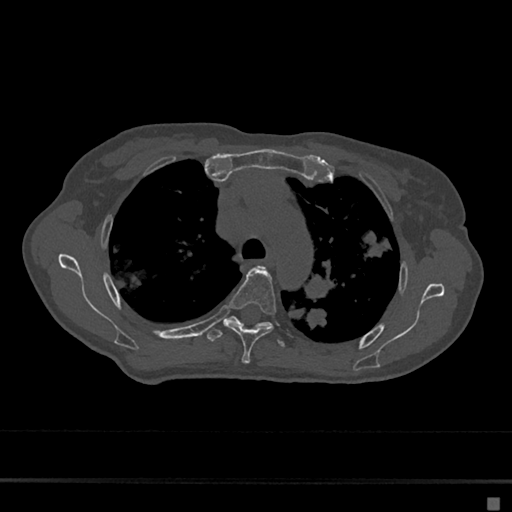
CT including the spine, one axial slice; slice 492 of 797 in the series (ordered by position); reconstruction kernel Br40s/3; bone window (W 1800 / L 400 HU); 0.5 mm slice thickness; 512 × 512 image matrix, field of view 360 × 360 mm. Female patient, age 68 years. Case-level facts recorded for this patient, not image findings: primary cancer: renal.
Outlined on this slice (semi-automatically segmented with operator editing):
- T4 vertebra: bounding box [x1, y1, x2, y2] px = [224, 268, 276, 364]
- T5 vertebra: [207, 316, 286, 347]